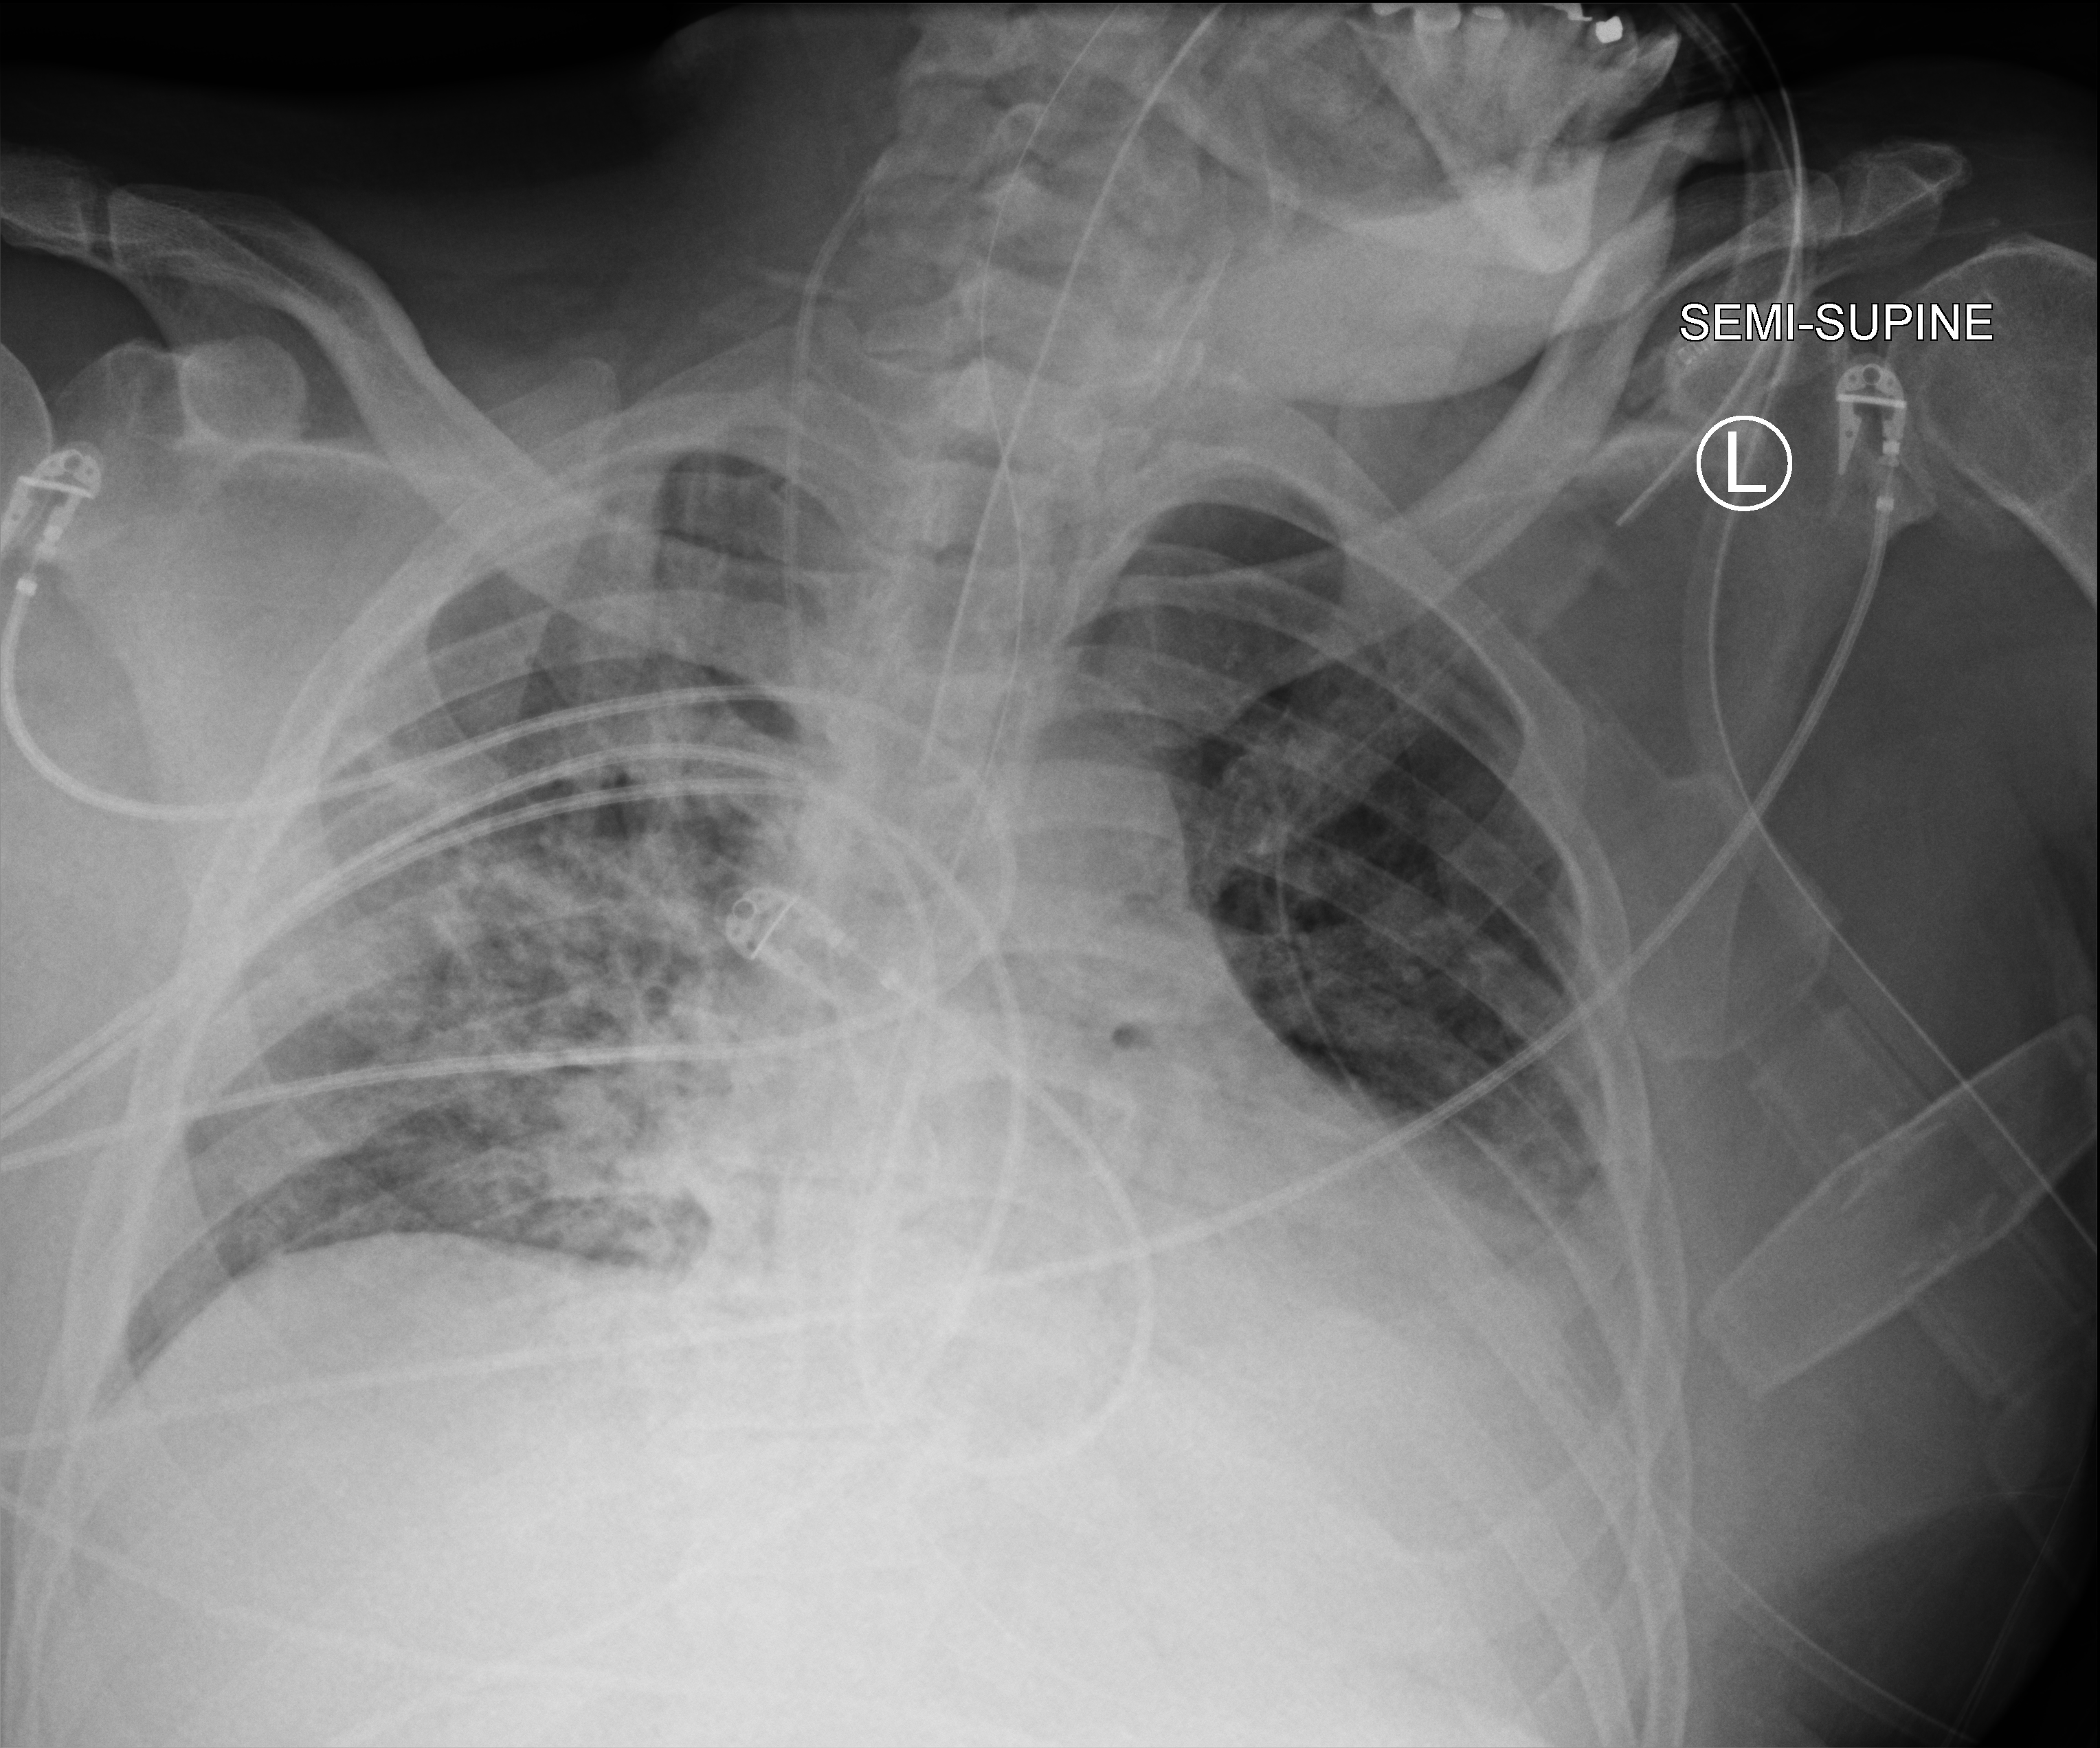
Bedside chest radiograph (computed radiography), anteroposterior (AP) projection. Patient hospitalised with COVID-19; male, aged 18–59 years.
Admission-level facts for this patient (not findings on this image; timing relative to this image not recorded): mechanically ventilated during this hospital stay: yes; chronic kidney disease (admission record): no.